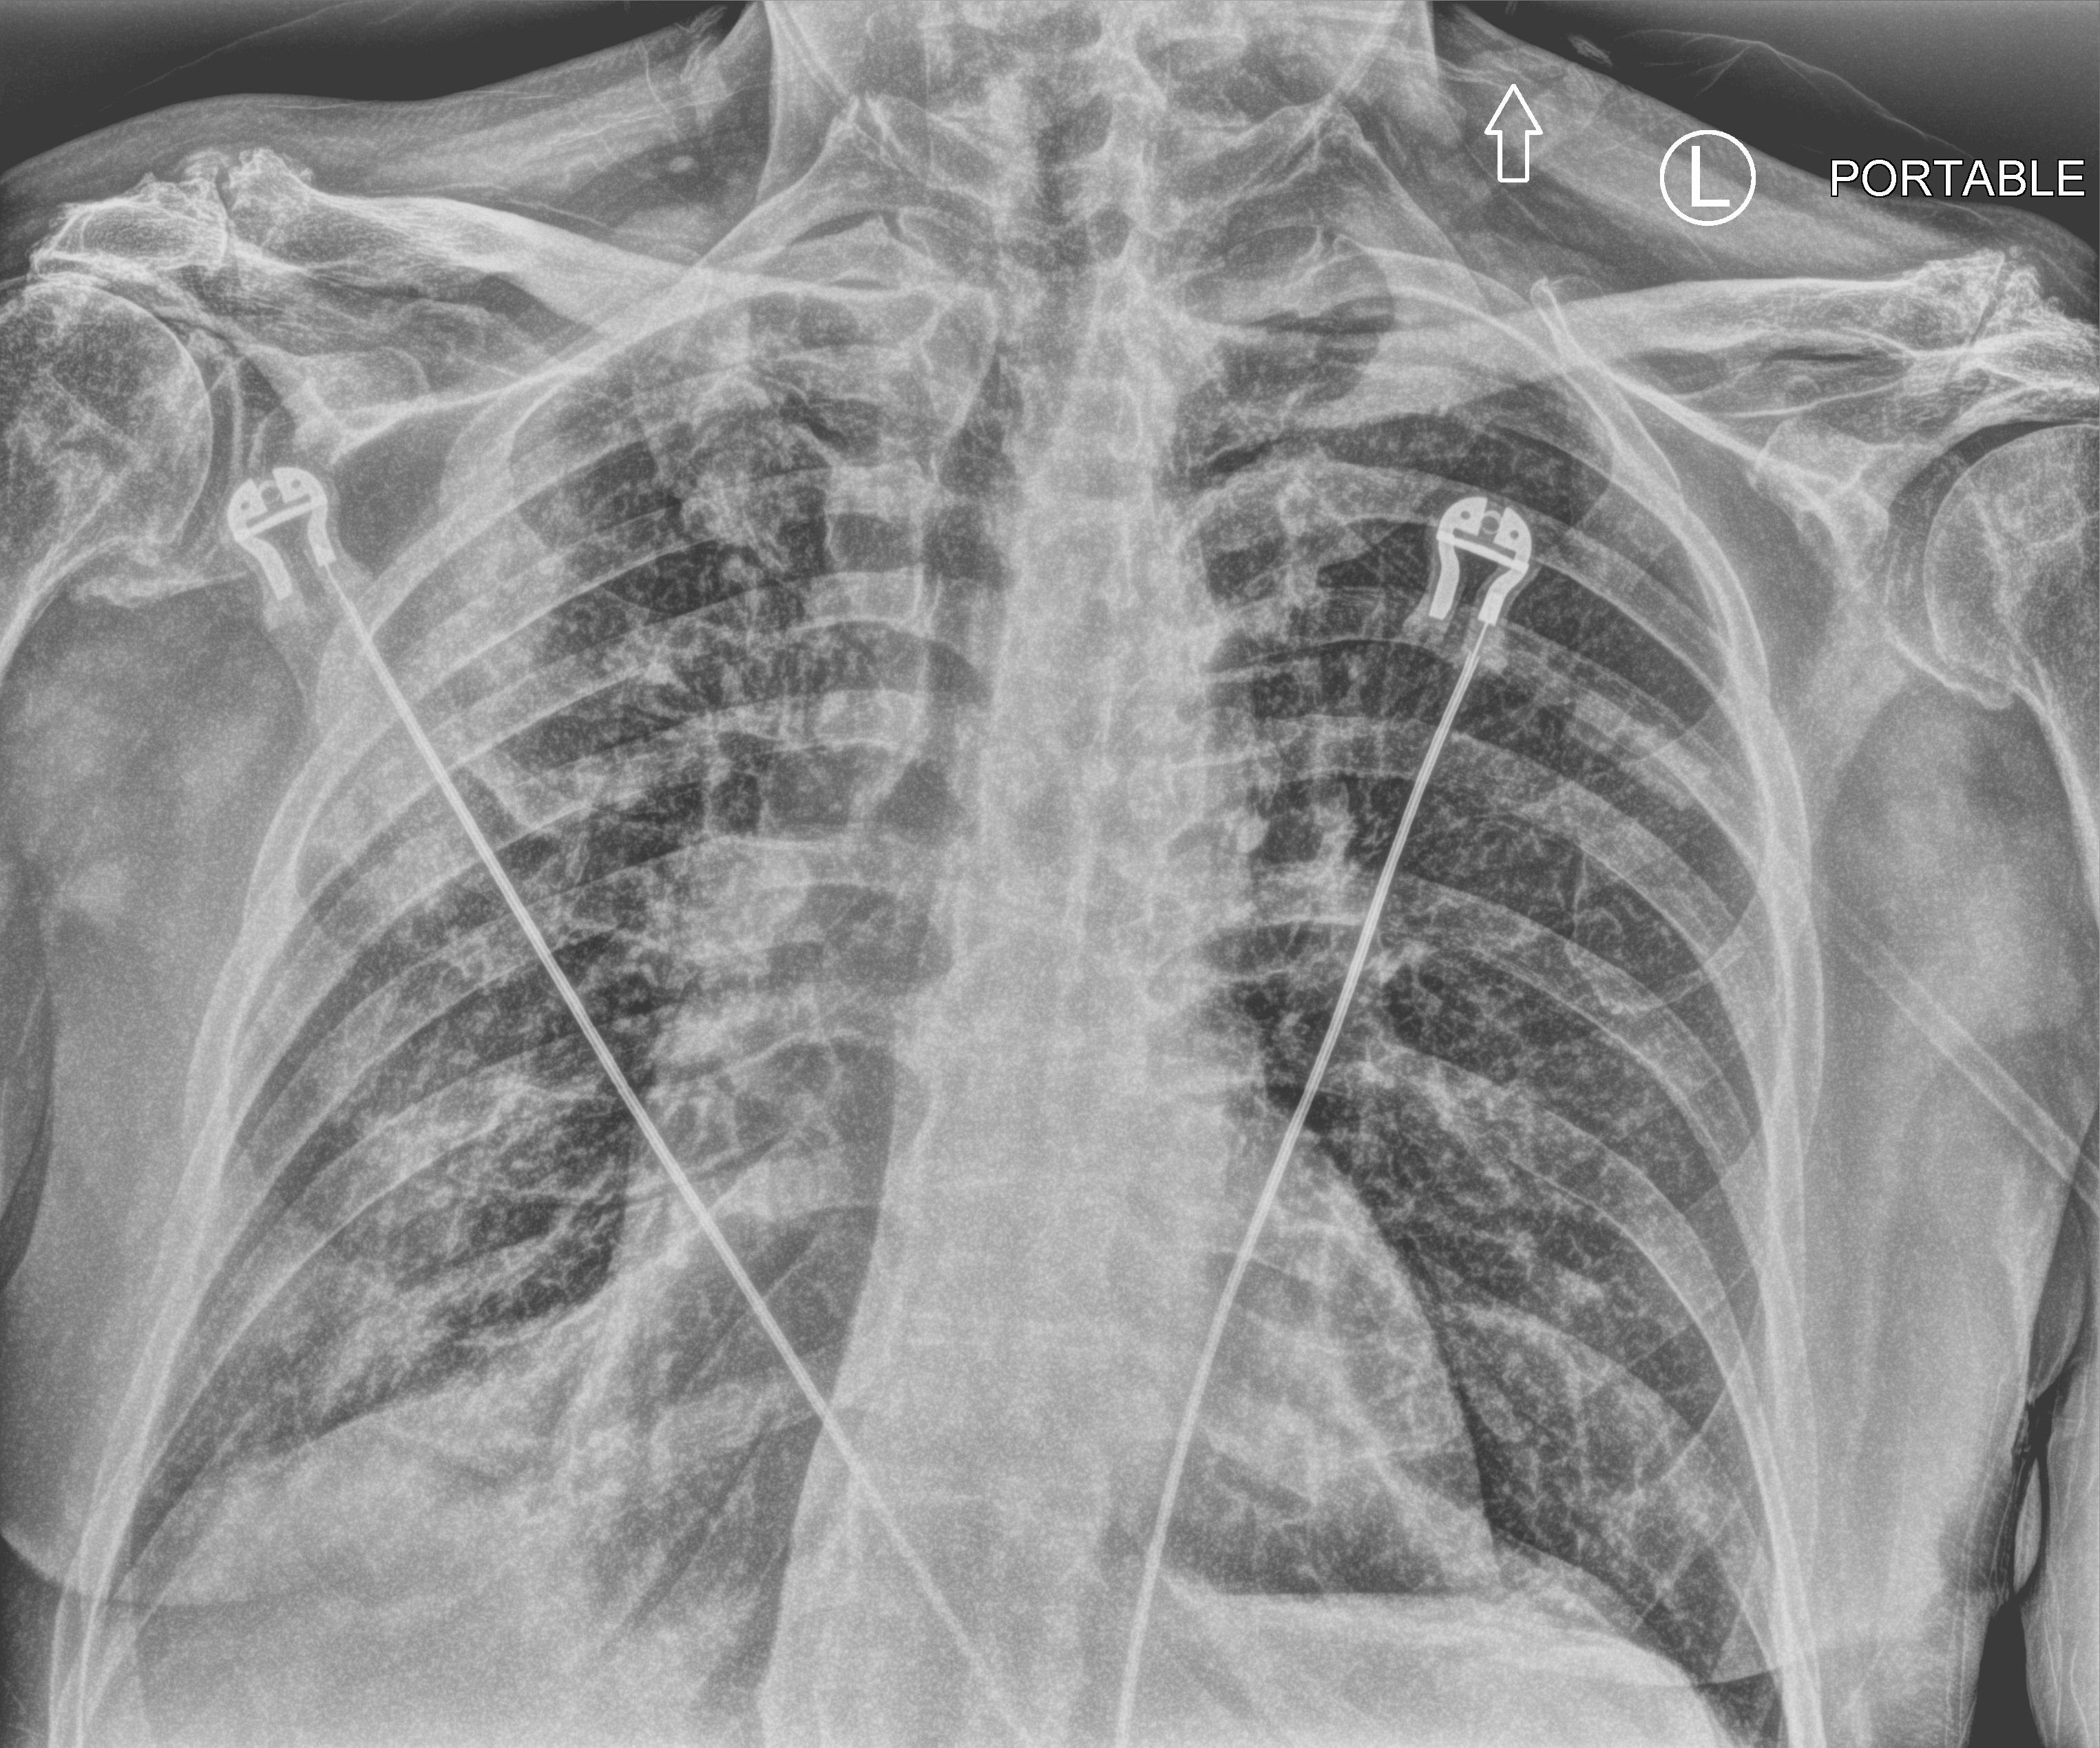
Bedside chest radiograph (computed radiography), anteroposterior (AP) projection. Male patient hospitalised with COVID-19, age 75–90 years.
From the hospital-stay record, not from the radiograph (when in the stay this image was taken is not recorded): hypertension (admission record): yes; length of hospital stay: 15 days; mechanically ventilated during this hospital stay: no.